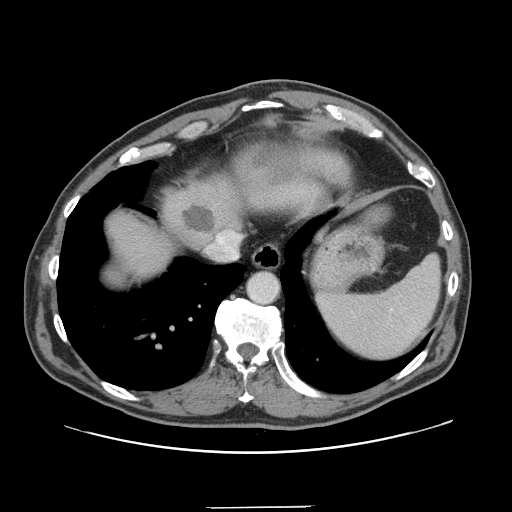
Contrast-enhanced abdominal CT, one axial slice; position 127 of 139 along the scan axis; soft-tissue window (W 400 / L 40 HU); 2.5 mm slice thickness; 512 × 512 image matrix. Male patient, age 64 years. From the clinical record (not read from this slice): diagnosis: colorectal cancer liver metastases, imaged before liver resection; multiple liver metastases: yes; largest metastasis: 3.5 cm.
Annotated regions visible in this slice (outlined manually by an expert reader):
- liver: box from (x=108, y=153) to (x=255, y=280) px
- planned liver remnant (the part of the liver to remain after resection): (x=108, y=171)–(x=247, y=279)
- liver metastasis: (x=183, y=209)–(x=215, y=235)